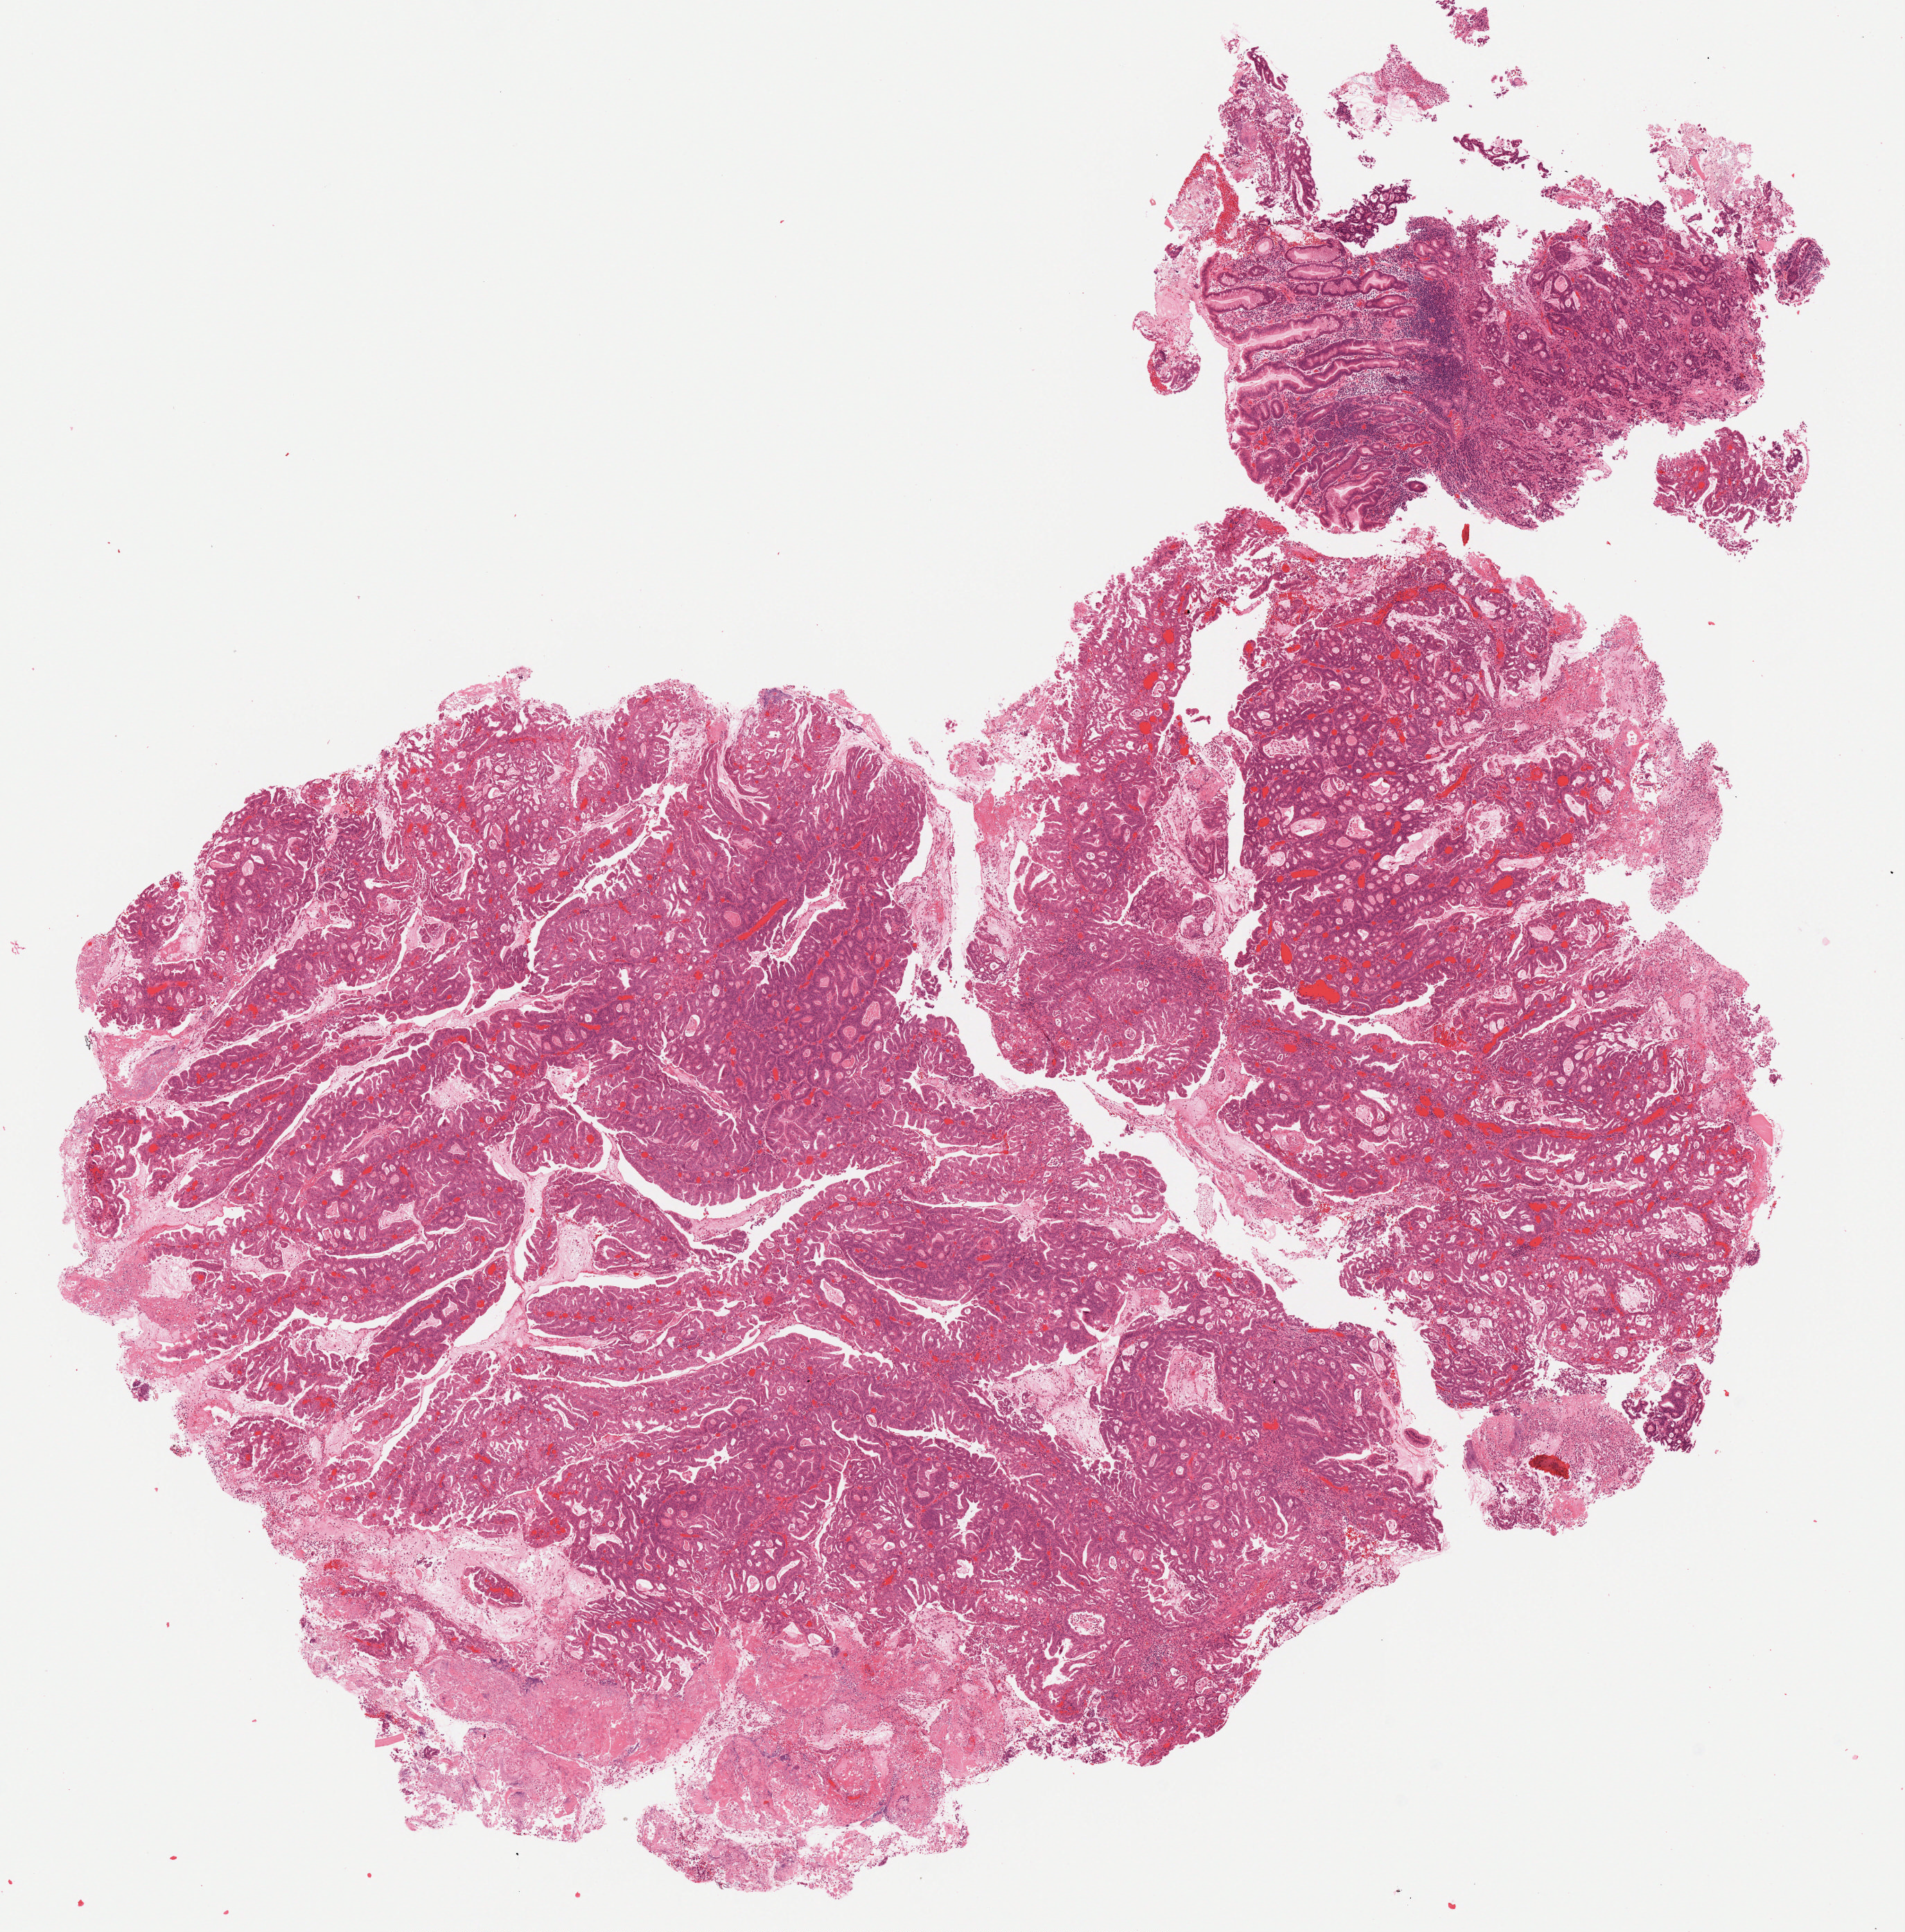
Whole-slide histology image, H&E-stained — a low-resolution overview of the entire scanned area, about 11.0 x 11.2 mm (acquisition: 20x scan); formalin-fixed paraffin-embedded (FFPE) diagnostic section; stomach, primary tumour sample. Female, age 75 years at initial diagnosis. Histologic grade: G3 (poorly differentiated).
Pathologic diagnosis: Mucinous adenocarcinoma (gastric antrum). TNM: T4a N3a M0. AJCC pathologic stage: IIIC.